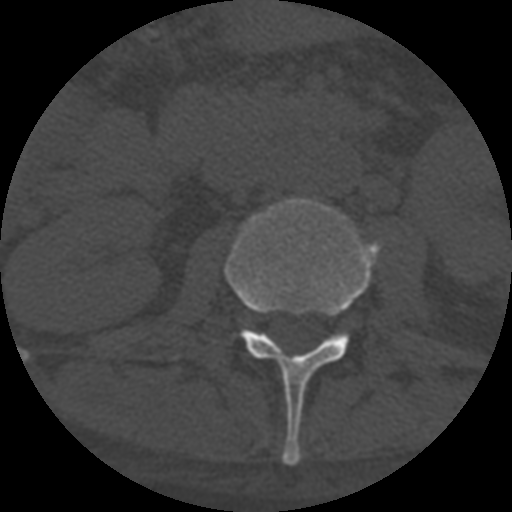
CT including the spine, one axial slice. Slice 257 of 708 in the series (ordered by position). Reconstruction kernel STANDARD. 120 kVp. One of 3 acquisitions stored at this slice position. Bone window (W 1800 / L 400 HU). 512 × 512 image matrix. Patient age 55 years. From the clinical record (not read from this slice): primary cancer: colon; vertebrae with lytic lesions (as recorded): T12, L1, L5.
Annotated regions visible in this slice (semi-automatic segmentation, software-assisted and operator-edited):
- L2 vertebra: box from (x=225, y=198) to (x=381, y=466) px